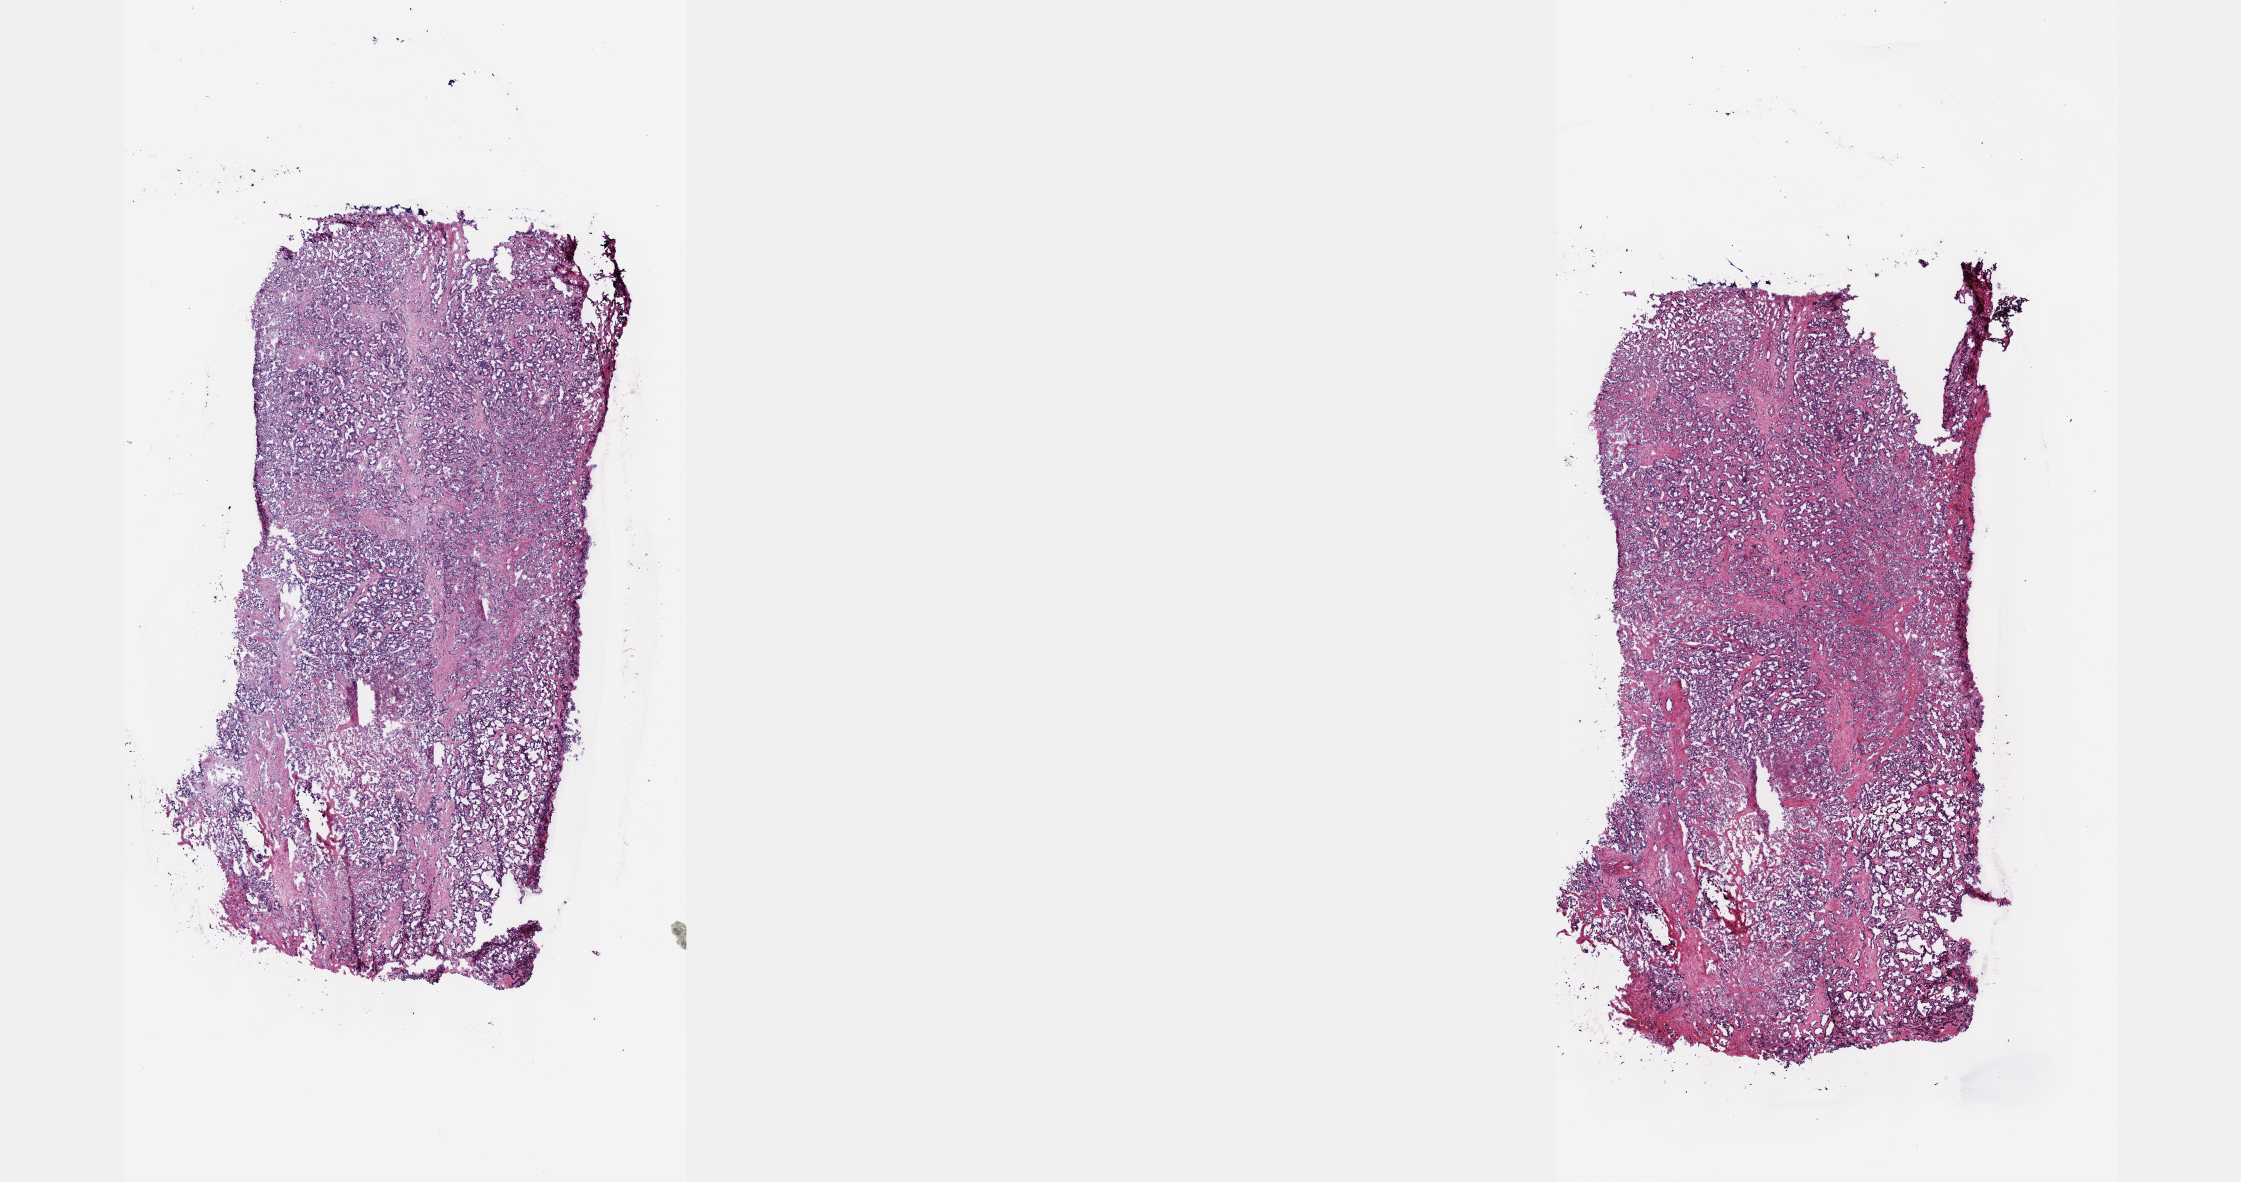
Digitized H&E tissue section (whole slide) — a low-resolution overview of the entire scanned area, about 18.1 x 9.6 mm; frozen section from the top of the tissue portion; sample: primary tumour, bile duct. Female patient; age at initial diagnosis 75 years. Histologic grade: G2 (moderately differentiated). Composition of this section per pathologist review: tumour cells 95%, tumour nuclei 70%, normal cells 0%, stromal cells 0%, necrosis 5%. Infiltration values recorded for this section: lymphocyte infiltration 4%, monocyte infiltration 0%, neutrophil infiltration 0%.
Pathologic diagnosis: Cholangiocarcinoma (intrahepatic bile duct). AJCC pathologic stage: I (7th edition).